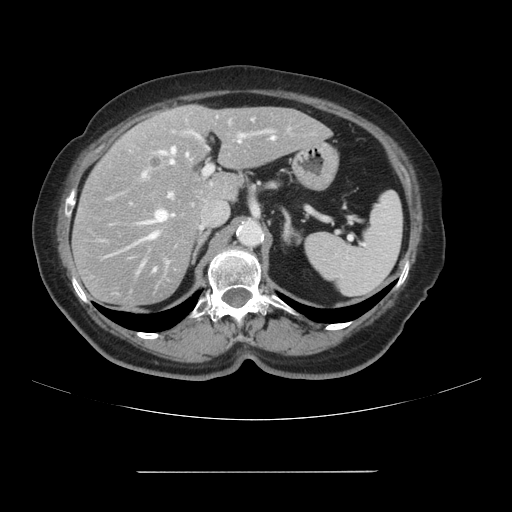
Contrast-enhanced abdominal CT, one axial slice. Position 64 of 111 along the scan axis. Intravenous contrast given. Soft-tissue window (W 400 / L 40 HU). 512 × 512 image matrix. Female patient, age 74 years. From the clinical record (not read from this slice): diagnosis: colorectal cancer liver metastases, imaged before liver resection; multiple liver metastases: yes; largest metastasis: 1.1 cm; disease in both lobes: yes.
Structures marked on this image (manually delineated by an expert):
- hepatic veins: box from (x=104, y=137) to (x=275, y=267) px
- liver: (x=74, y=106)–(x=329, y=308)
- planned liver remnant (the part of the liver to remain after resection): (x=148, y=106)–(x=329, y=200)
- portal vein (with intrahepatic branches): (x=141, y=116)–(x=317, y=199)
- liver metastasis: (x=151, y=158)–(x=159, y=165)